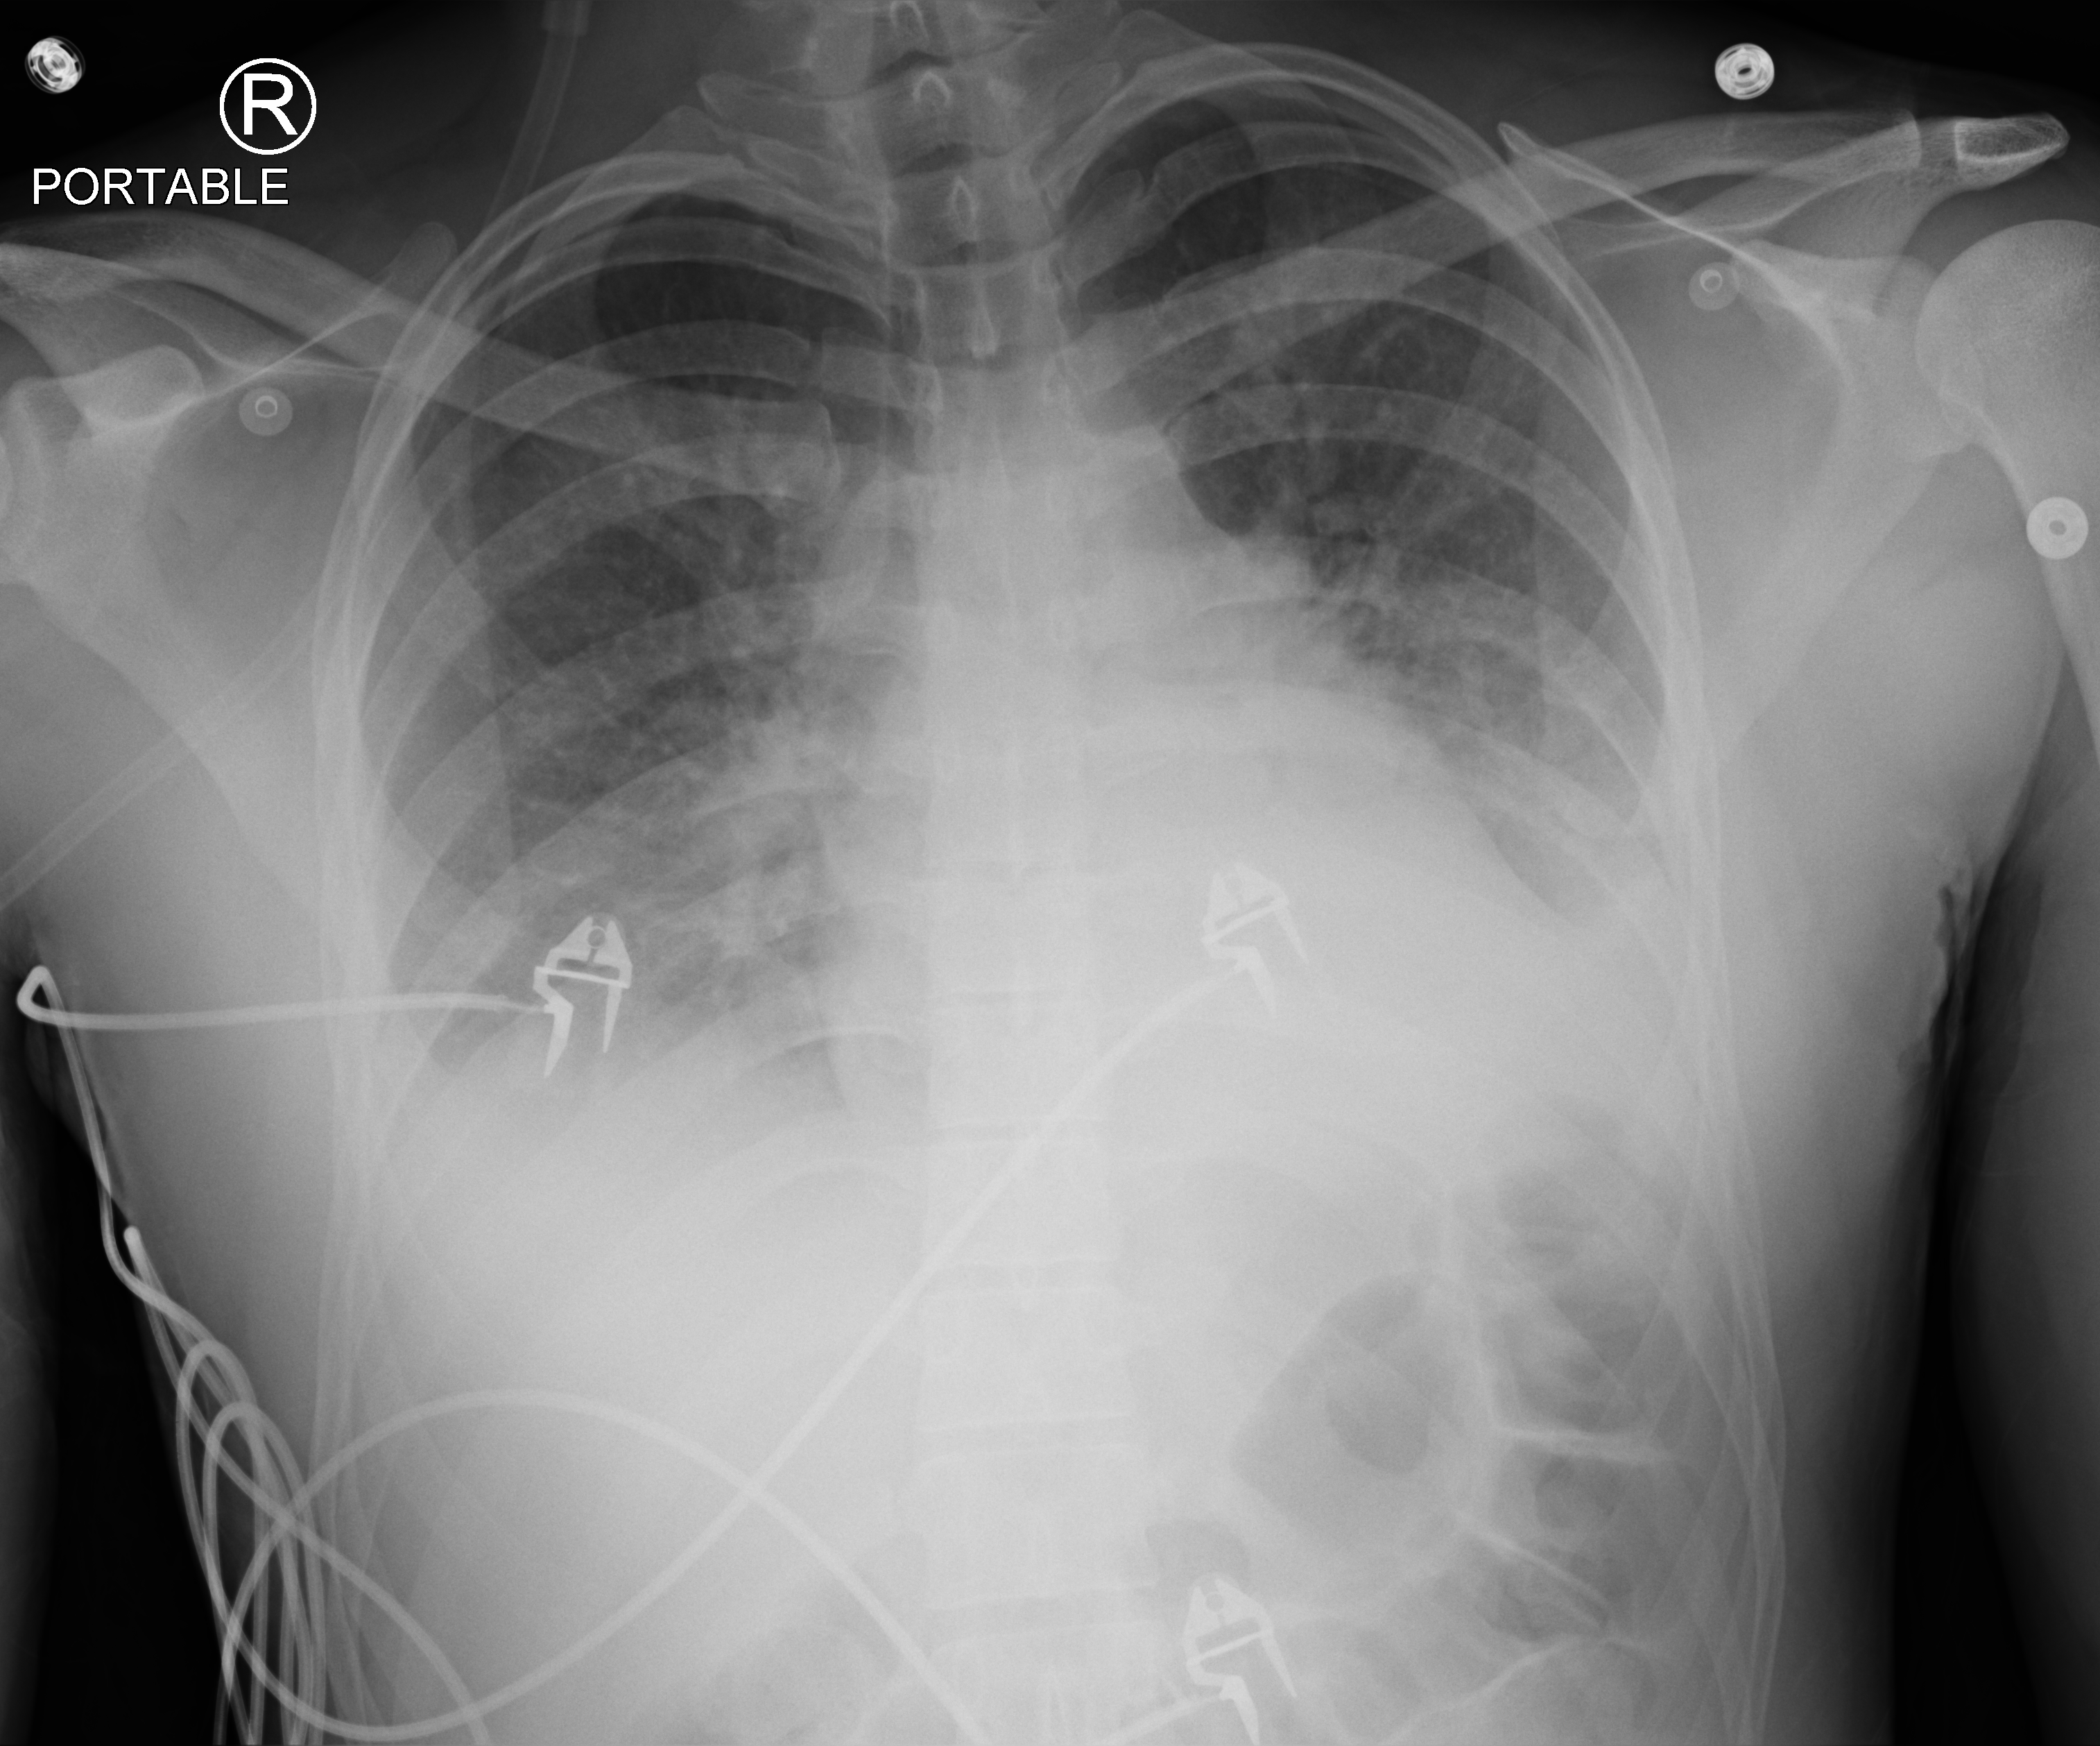
Portable chest radiograph. Male patient hospitalised with COVID-19, age 18–59 years.
Hospital-stay facts (about this admission, not read from this image; timing relative to this image not recorded): mechanically ventilated during this hospital stay: no; admitted to intensive care during this hospital stay: no.